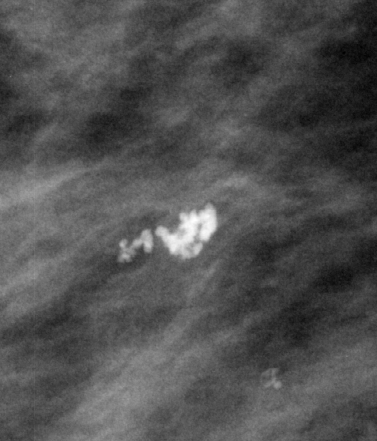
Region of interest cut from a scanned film mammogram (one marked finding), right breast, MLO view.
Marked abnormality: calcifications, morphology pleomorphic, distribution clustered; BI-RADS assessment category 4; subtlety rating 5 on a 1 (subtle) to 5 (obvious) scale; pathology (as recorded): benign.